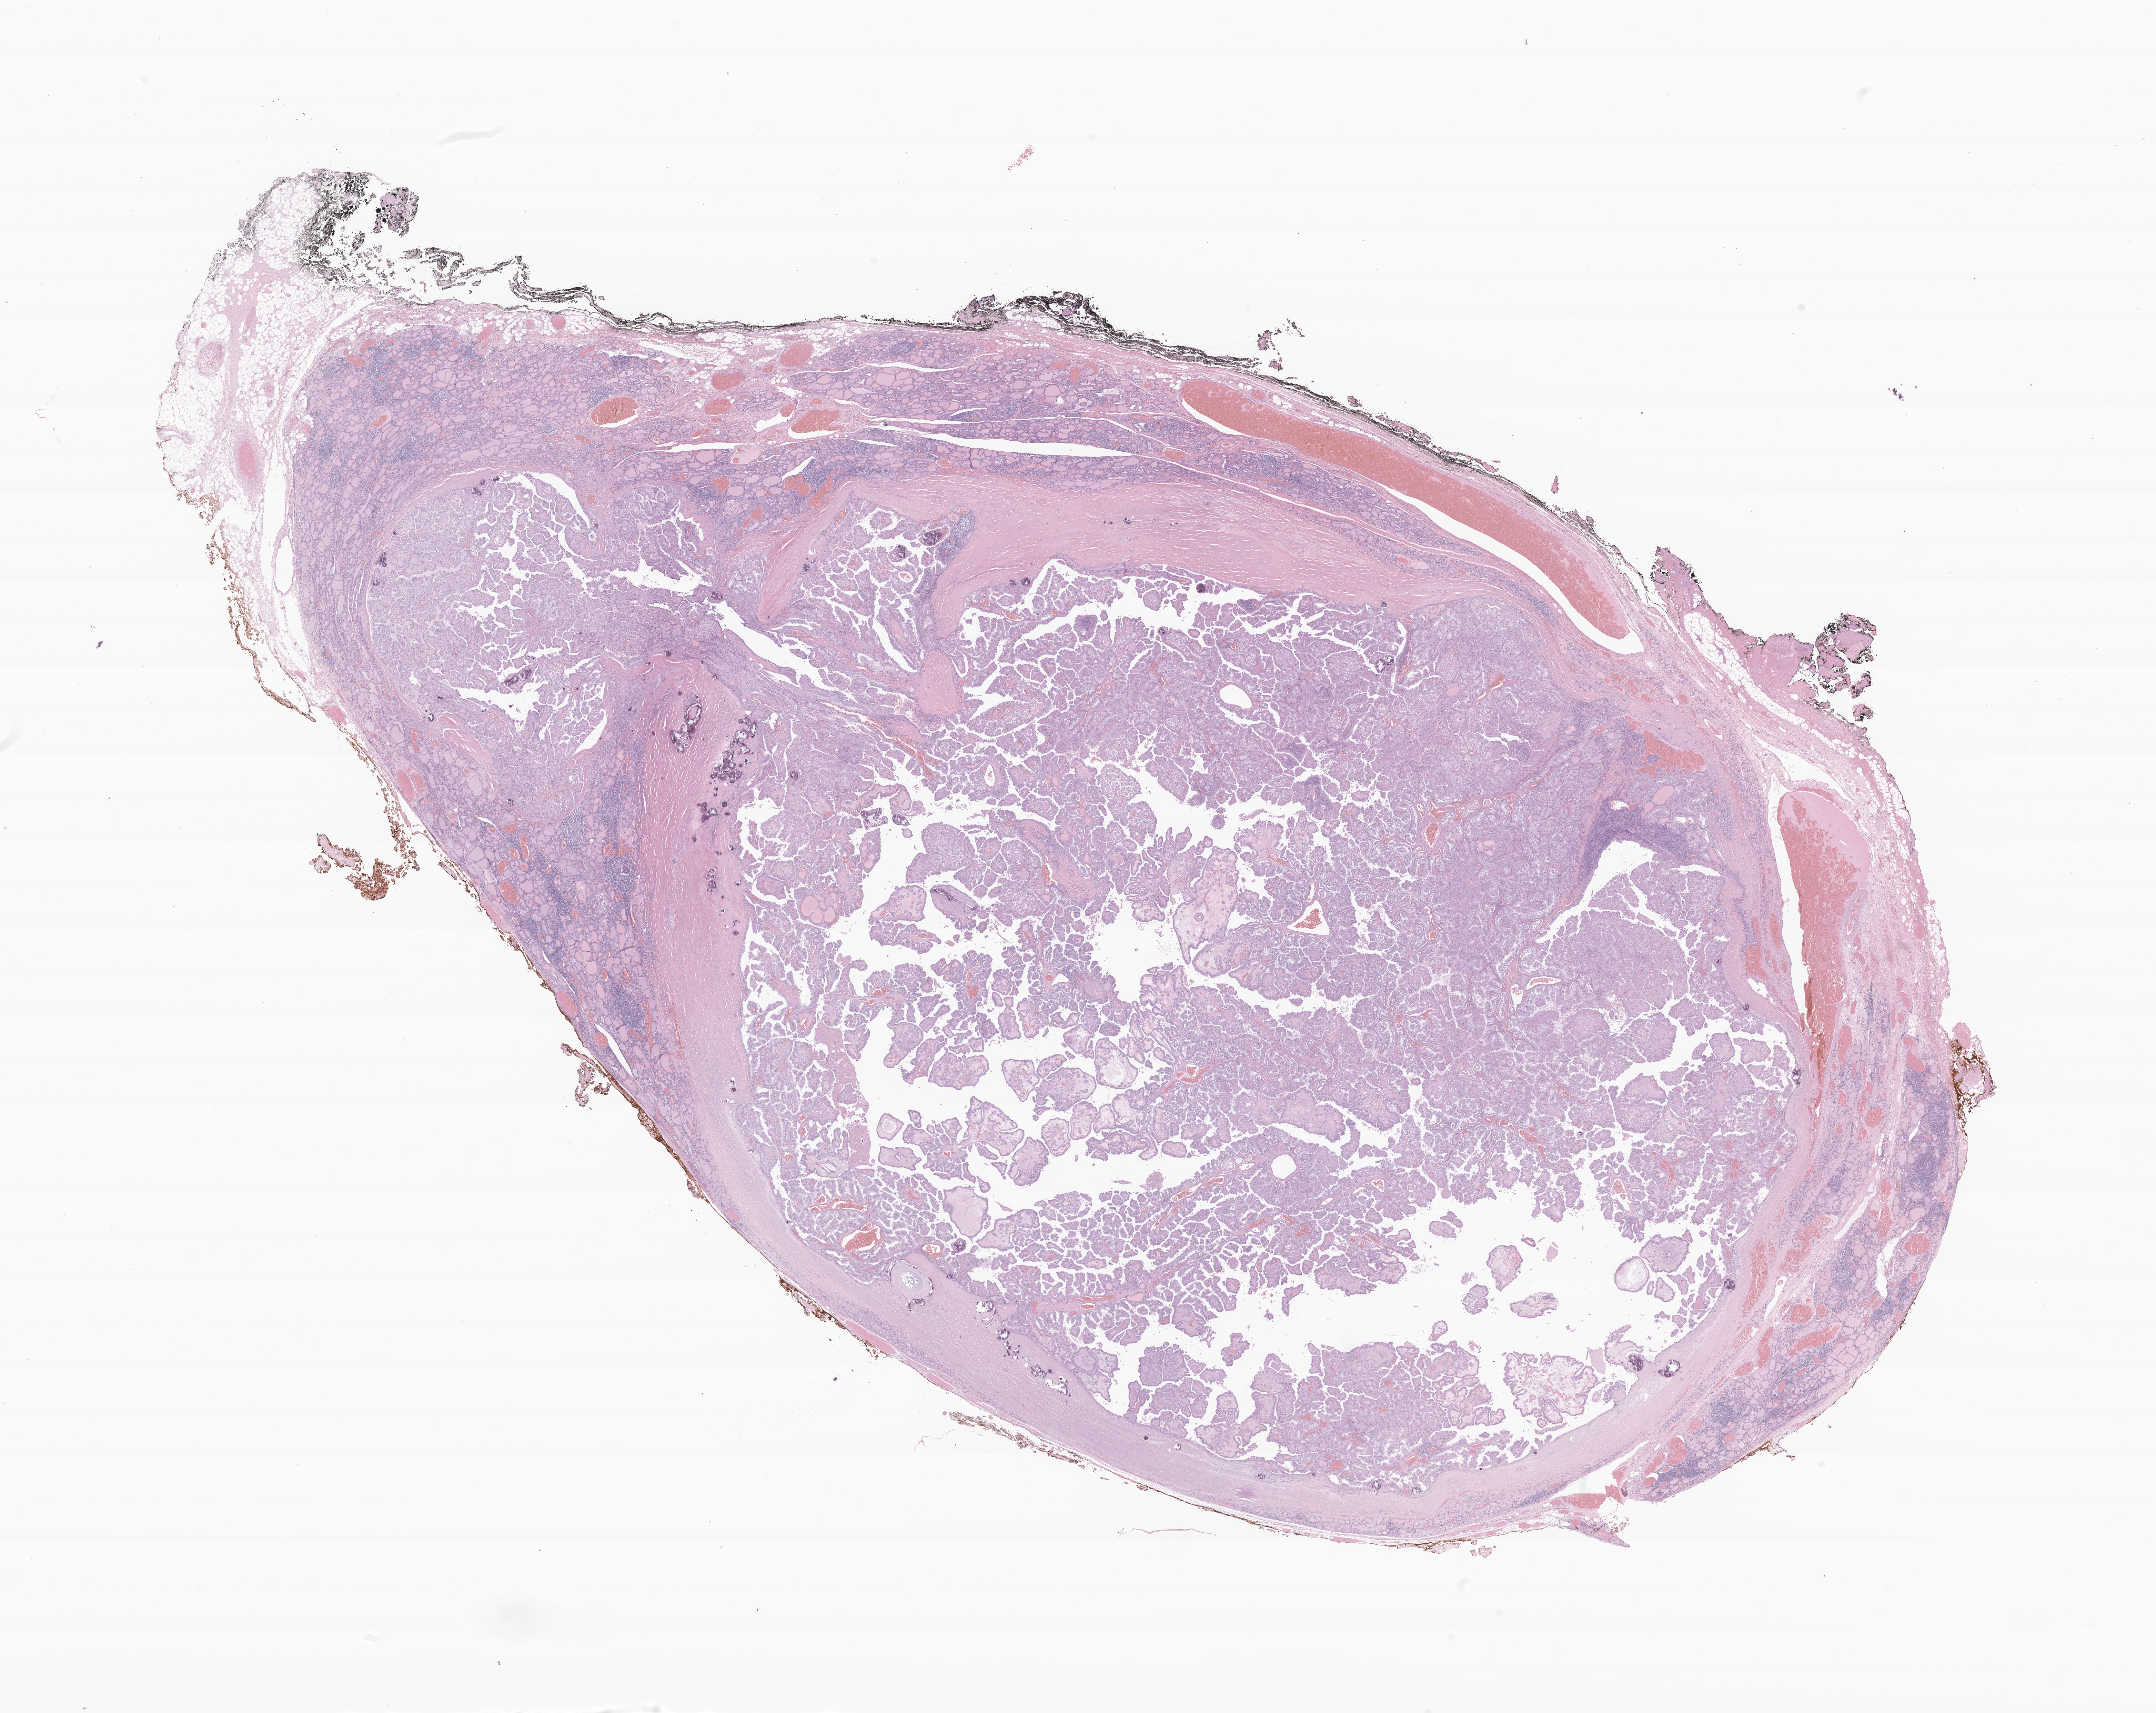
Haematoxylin and eosin whole-slide image of tumor tissue from the thyroid — shown as a low-resolution overview of the whole scanned area (about 26.3 x 20.9 mm), FFPE section. Female patient, age 214 months (17 years 10 months).
Diagnosis (ICD-O-3 morphology term): Papillary carcinoma, NOS.